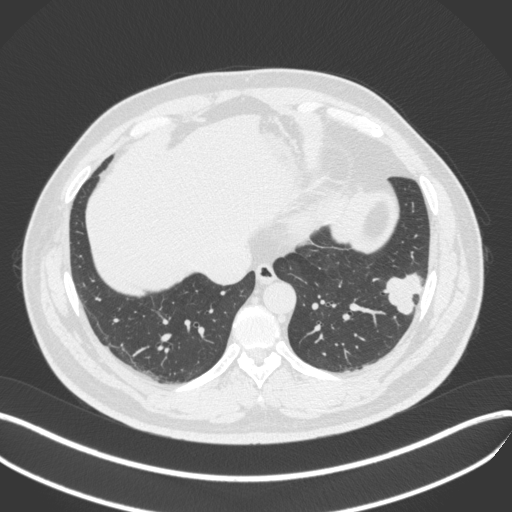
Chest CT, one axial slice. Position 123 of 420 along the scan axis. 120 kVp. Lung window (W 1500 / L -600 HU). 1 mm slice thickness. 512 × 512 image matrix, field of view 400 × 400 mm. Patient: male, 39 years. From the clinical record (not read from this slice): clinical TNM (as recorded): T2a N0 M0; histopathological grade: G2-3.
Structures marked on this image (rectangle marked by the reading radiologist):
- lung tumour (recorded histology: adenocarcinoma): box from (x=379, y=267) to (x=431, y=319) px